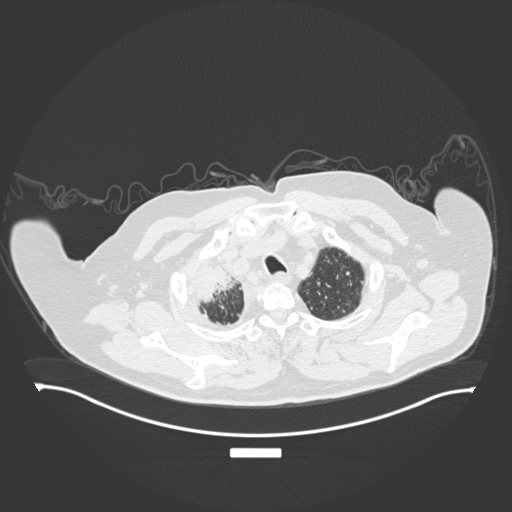
Chest CT, one axial slice. Position 171 of 201 along the scan axis. Lung window (W 1500 / L -600 HU). 1 mm slice thickness. 512 × 512 image matrix, field of view 500 × 500 mm. Patient: male, 69 years. Case-level facts recorded for this patient, not image findings: clinical TNM (as recorded): T4 N3 M1.
Annotated regions visible in this slice (rectangle marked by the reading radiologist):
- lung tumour (recorded histology: adenocarcinoma): box from (x=187, y=256) to (x=244, y=310) px